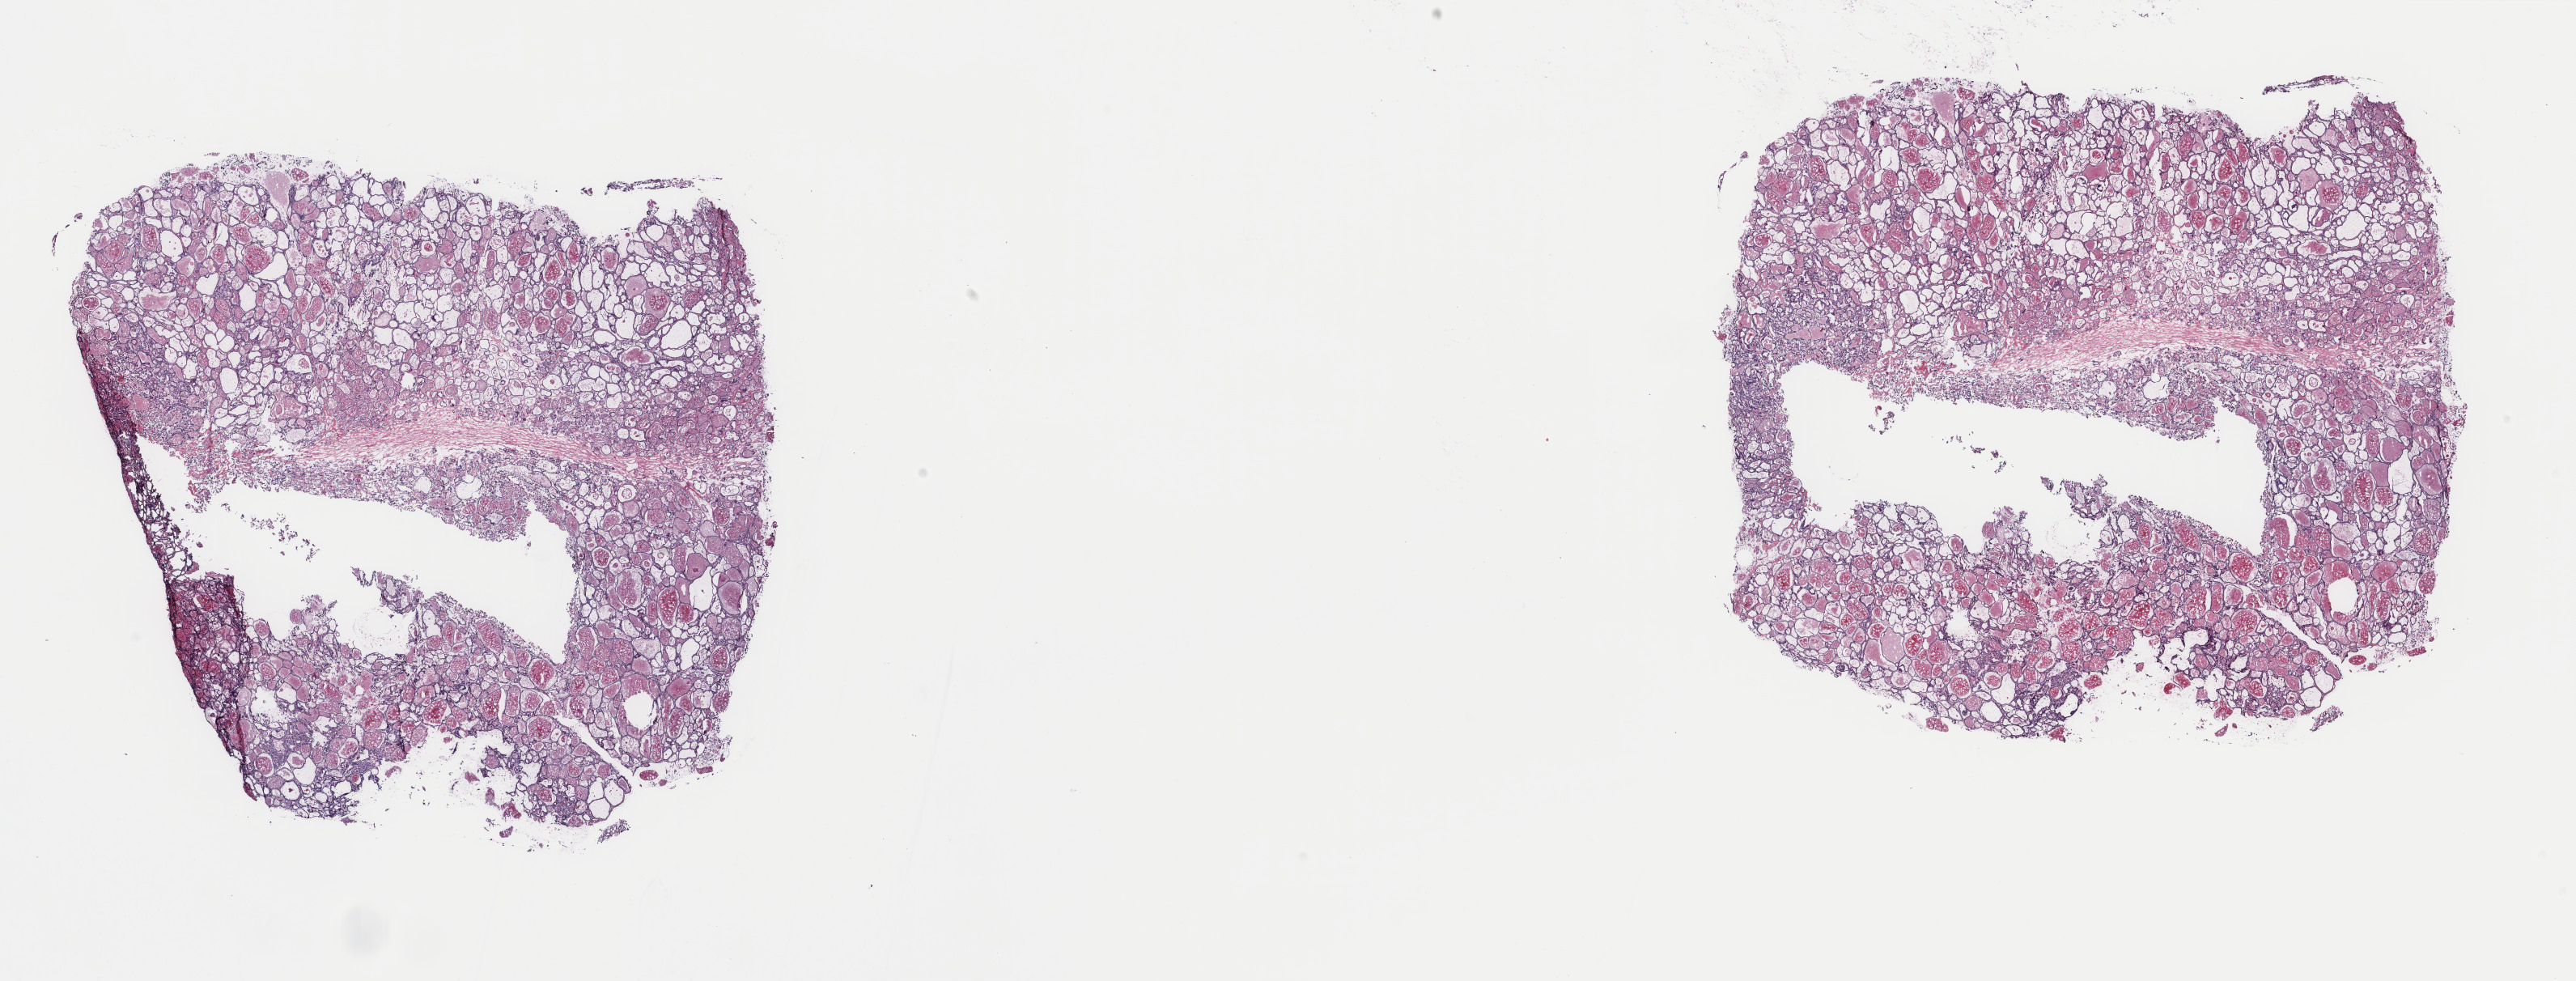
Digitized H&E-stained tissue section (whole slide), a low-resolution overview of the entire scanned area, about 25.3 x 9.6 mm. Frozen section from the top of the tissue portion. Thyroid, primary tumour sample. Patient: female, age at initial diagnosis 49 years. Composition of this section per pathologist review: tumour cells 95%, tumour nuclei 99%.
Pathologic diagnosis: Papillary carcinoma, follicular variant (thyroid gland).